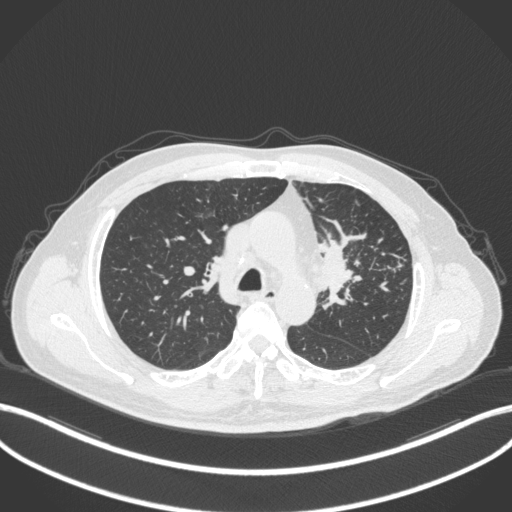
Chest CT, one axial slice. Position 239 of 386 along the scan axis. Lung window (W 1500 / L -600 HU). 1 mm slice thickness. 512 × 512 image matrix, field of view 400 × 400 mm. Male patient, age 69 years. Case-level facts recorded for this patient, not image findings: clinical TNM (as recorded): T2a N2 M0; histopathological grade: G2-3.
Annotated regions visible in this slice (rectangle marked by the reading radiologist):
- lung tumour (recorded histology: adenocarcinoma): bounding box (x1, y1, x2, y2) in pixels: (323, 233, 357, 311)